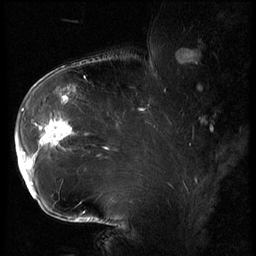
Breast MRI (dynamic contrast-enhanced), one sagittal slice. Slice 43 of 62 in the series (ordered by position). 3 images stored at this slice position (order not interpretable as contrast timing). 1.5 T. TE 4.2 ms, TR 9 ms. 2.5 mm slice thickness. 256 × 256 image matrix, field of view 180 × 180 mm. Female patient, age 43 years. From the clinical record (not read from this slice): setting: breast cancer imaged before/during neoadjuvant chemotherapy; receptor status: HER2-positive.
Outlined on this slice (semi-automatically segmented with operator editing):
- analysis volume of interest (the breast-tissue region the enhancement analysis was run in; not a lesion): bounding box <16,90,82,203> (left, top, right, bottom; pixels)
- tumour enhancement mask (voxels above the 140 % enhancement threshold inside the analysis volume of interest): <16,96,75,197>